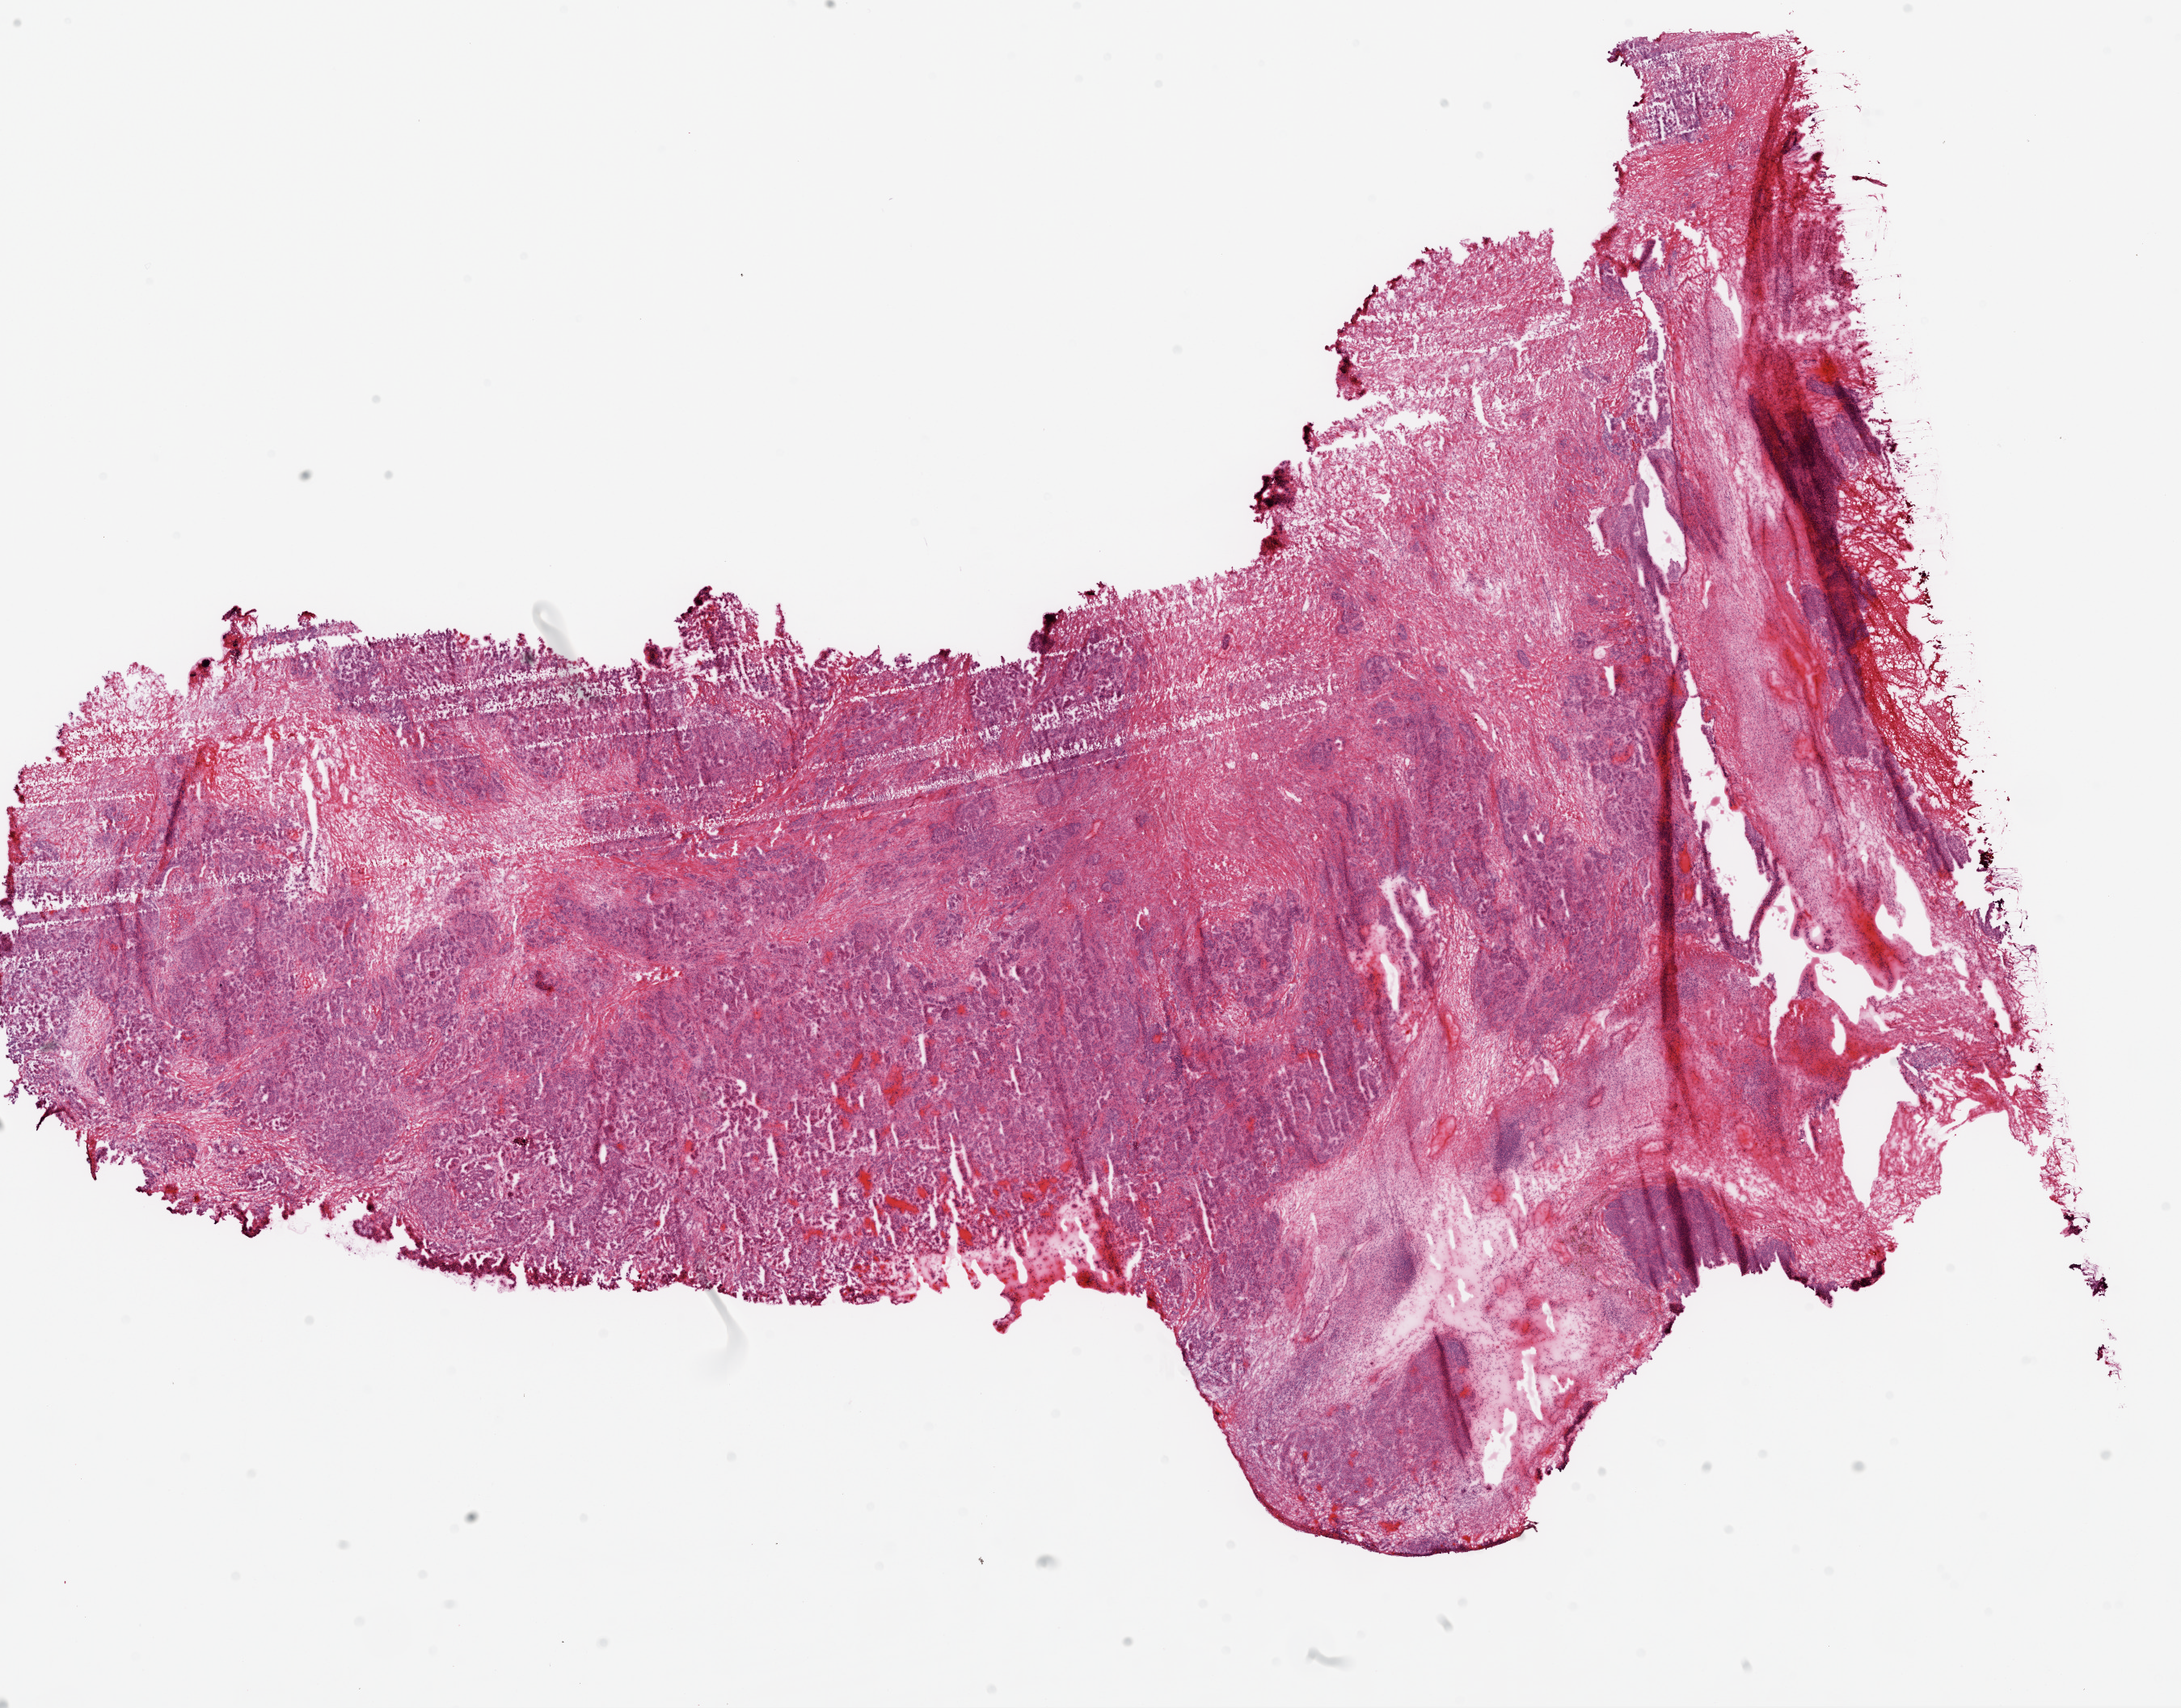
Digitized H&E tissue section (whole slide) — shown as a low-resolution overview of the whole scanned area (about 21.8 x 17.0 mm, acquisition: 20x scan). Frozen section from the top of the tissue portion. Primary tumour sample from the ovary. Female, age 61 years at initial diagnosis. Histologic grade: G3 (poorly differentiated). Slide review estimates, as recorded: tumour cells 75%, tumour nuclei 85%, stromal cells 20%, necrosis 5%.
Laterality: bilateral. Histologic diagnosis: Serous cystadenocarcinoma, NOS. FIGO stage: IIIC.